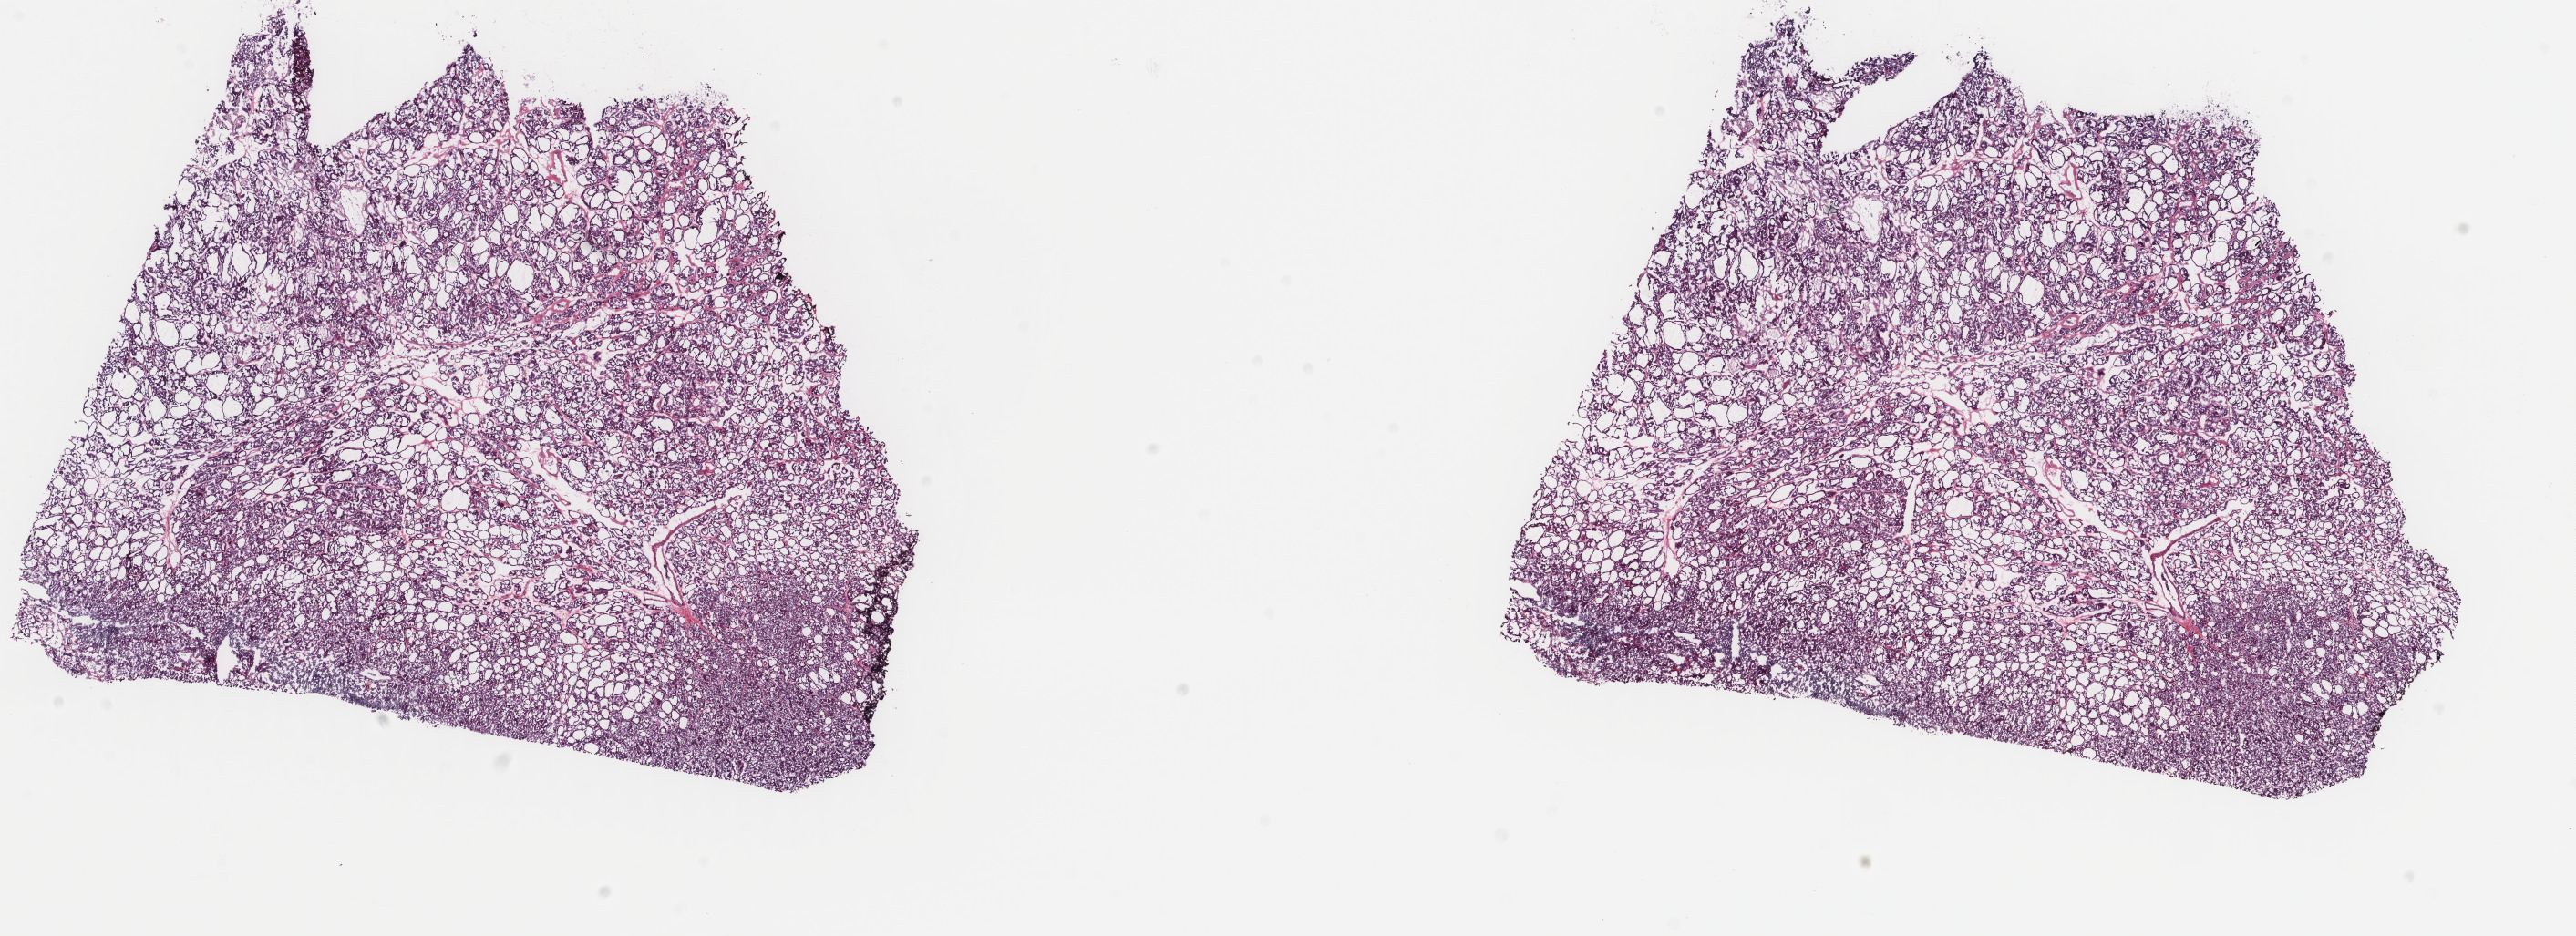
Digitized H&E-stained tissue section (whole slide) — whole scanned area (about 22.4 x 8.2 mm, slide scanned at 40x) shown as a low-resolution overview; frozen section from the top of the tissue portion; sample: primary tumour, thyroid. Patient: female, age at initial diagnosis 42 years. Composition of this section per pathologist review: tumour cells 80%, tumour nuclei 80%, normal cells 0%, stromal cells 20%, necrosis 0%. Inflammatory infiltration, as recorded: lymphocyte infiltration 1%, monocyte infiltration 0%, neutrophil infiltration 0%.
- histologic diagnosis: Papillary adenocarcinoma, NOS (thyroid gland)
- lymph nodes positive (case pathology): 0 of 3 examined
- AJCC pathologic stage: I